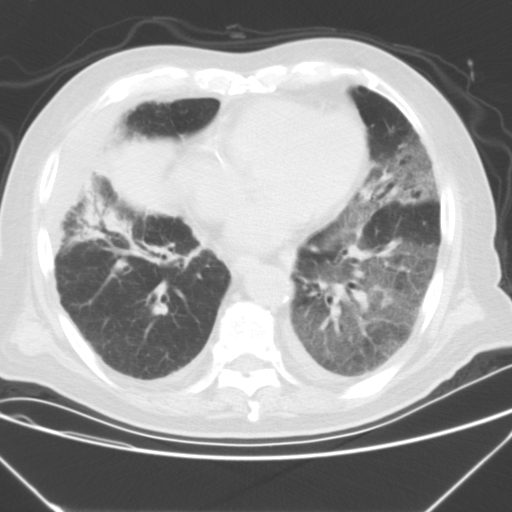
Chest CT, one axial slice; slice 11 of 43 in the series (ordered by position); 120 kVp; lung window (W 1500 / L -600 HU); 5 mm slice thickness; 512 × 512 image matrix. Patient: male, 85 years. Case-level facts recorded for this patient, not image findings: clinical TNM (as recorded): T4 N3 M2.
Annotated regions visible in this slice (bounding box drawn by a radiologist):
- lung tumour (recorded histology: squamous cell carcinoma): bounding box <92,136,184,226> (left, top, right, bottom; pixels)